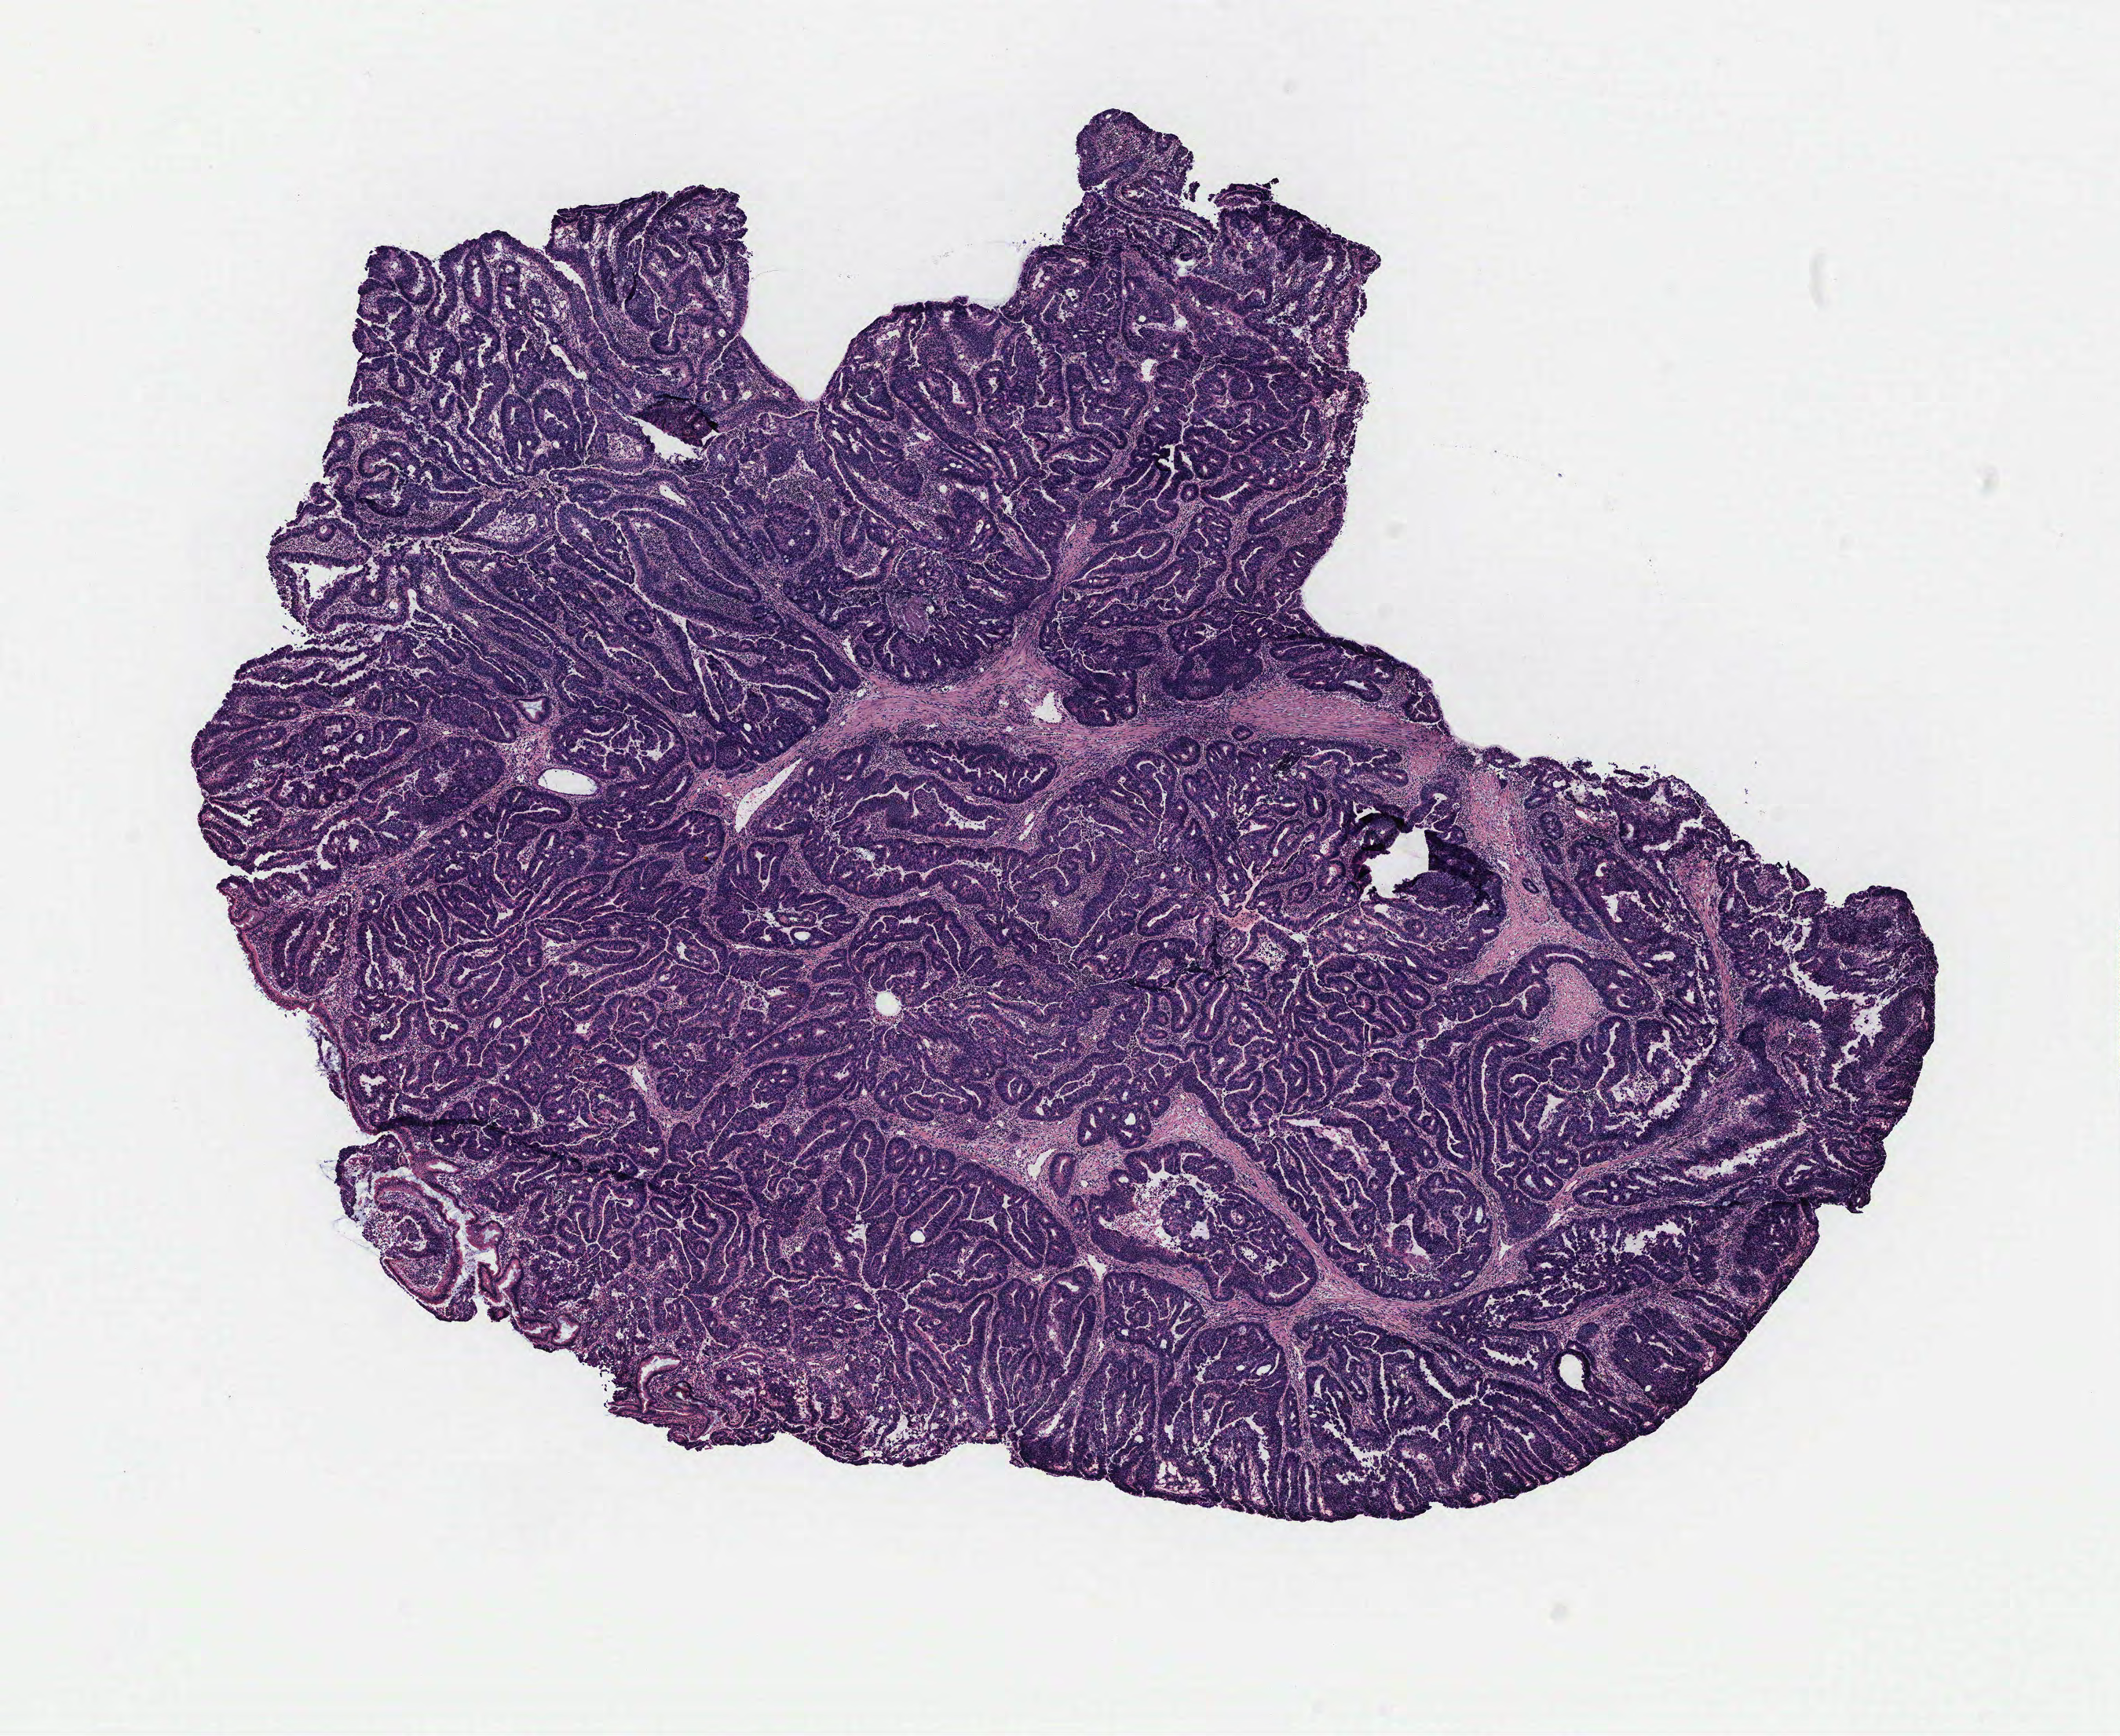
H&E-stained whole-slide image, low-resolution overview of the scanned area, about 10.8 x 8.8 mm (from a 40x scan), colon, normal (non-tumour) tissue. Male, 62 y/o.
This section: normal (non-tumour) tissue from the same patient. Patient diagnosis: Adenocarcinoma, NOS.